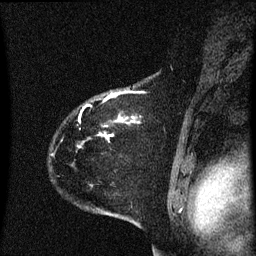
Breast MRI (dynamic contrast-enhanced), one sagittal slice. Slice 51 of 60 in the series (ordered by position). Dynamic contrast-enhanced series, image 2 of 3 at this slice position (ordered by acquisition). 1.5 T. TE 4.2 ms, TR 8.4 ms. 256 × 256 image matrix. Female patient, age 35 years. Case-level facts recorded for this patient, not image findings: setting: breast cancer imaged before/during neoadjuvant chemotherapy; receptor status: HER2-positive.
Outlined on this slice (semi-automatically segmented with operator editing):
- analysis volume of interest (the breast-tissue region the enhancement analysis was run in; not a lesion): bounding box <52,72,174,173> (left, top, right, bottom; pixels)
- tumour enhancement mask (voxels above the 70 % enhancement threshold inside the analysis volume of interest): <79,92,127,149>